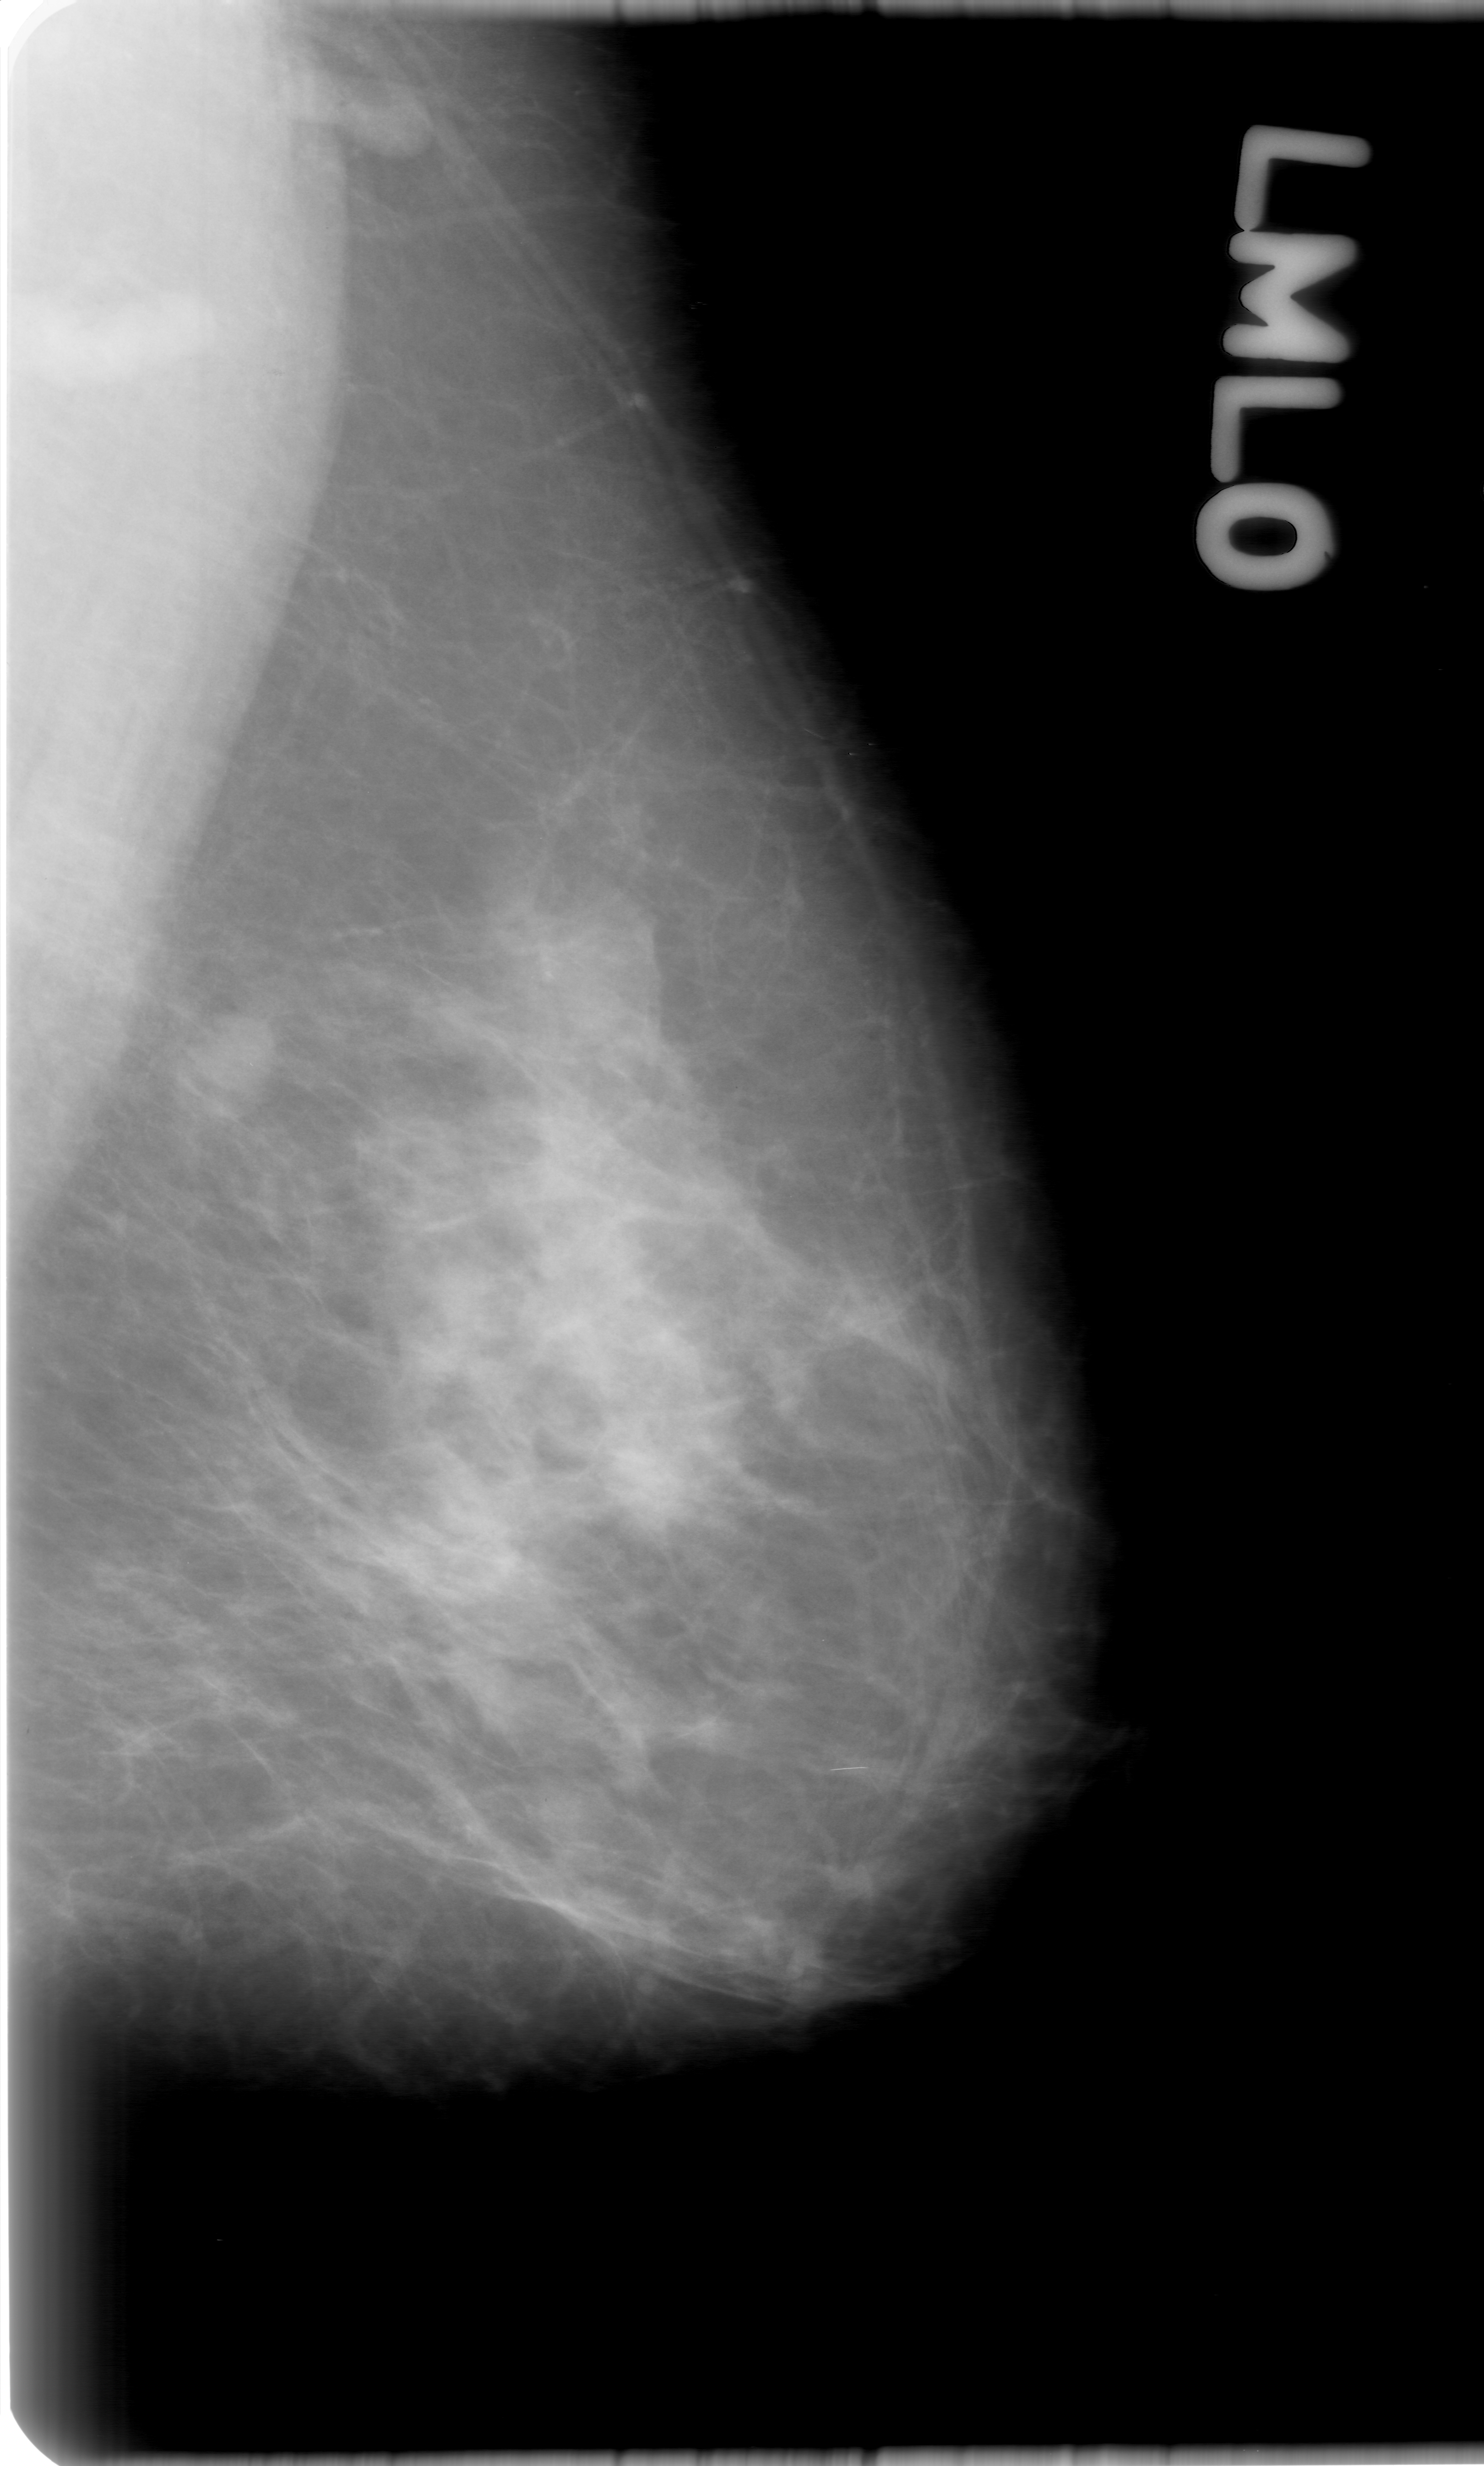
Scanned film-screen mammogram; left breast; mediolateral oblique (MLO) view; BI-RADS breast density category 2 (scale 1–4).
Finding: mass, shape oval, margins microlobulated; BI-RADS assessment category 0; pathology (as recorded): benign.